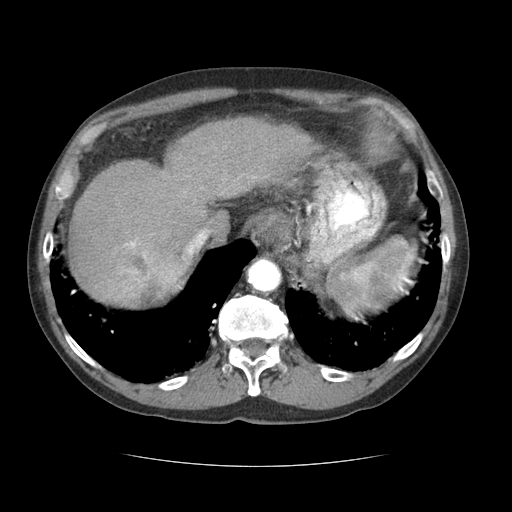
Contrast-enhanced abdominal CT (liver protocol), one axial slice; position 53 of 69 along the scan axis; 120 kVp; soft-tissue window (W 400 / L 40 HU); 2.5 mm slice thickness; 512 × 512 image matrix, field of view 360 × 360 mm. Case-level facts recorded for this patient, not image findings: diagnosis: hepatocellular carcinoma (patient treated with transarterial chemoembolisation; whether this scan precedes or follows treatment is not stated here); TNM stage (as recorded): Stage-II; Child-Pugh class: B; tumour differentiation: poorly differentiated; tumour nodularity: multinodular.
Structures marked on this image (semi-automatically segmented with operator editing):
- liver parenchyma outside the tumour (the mass and vessels are separate outlines, so this box may not span the whole liver): bounding box [x1, y1, x2, y2] px = [68, 116, 318, 300]
- mass: [97, 237, 187, 306]
- liver vessels: [134, 239, 196, 255]